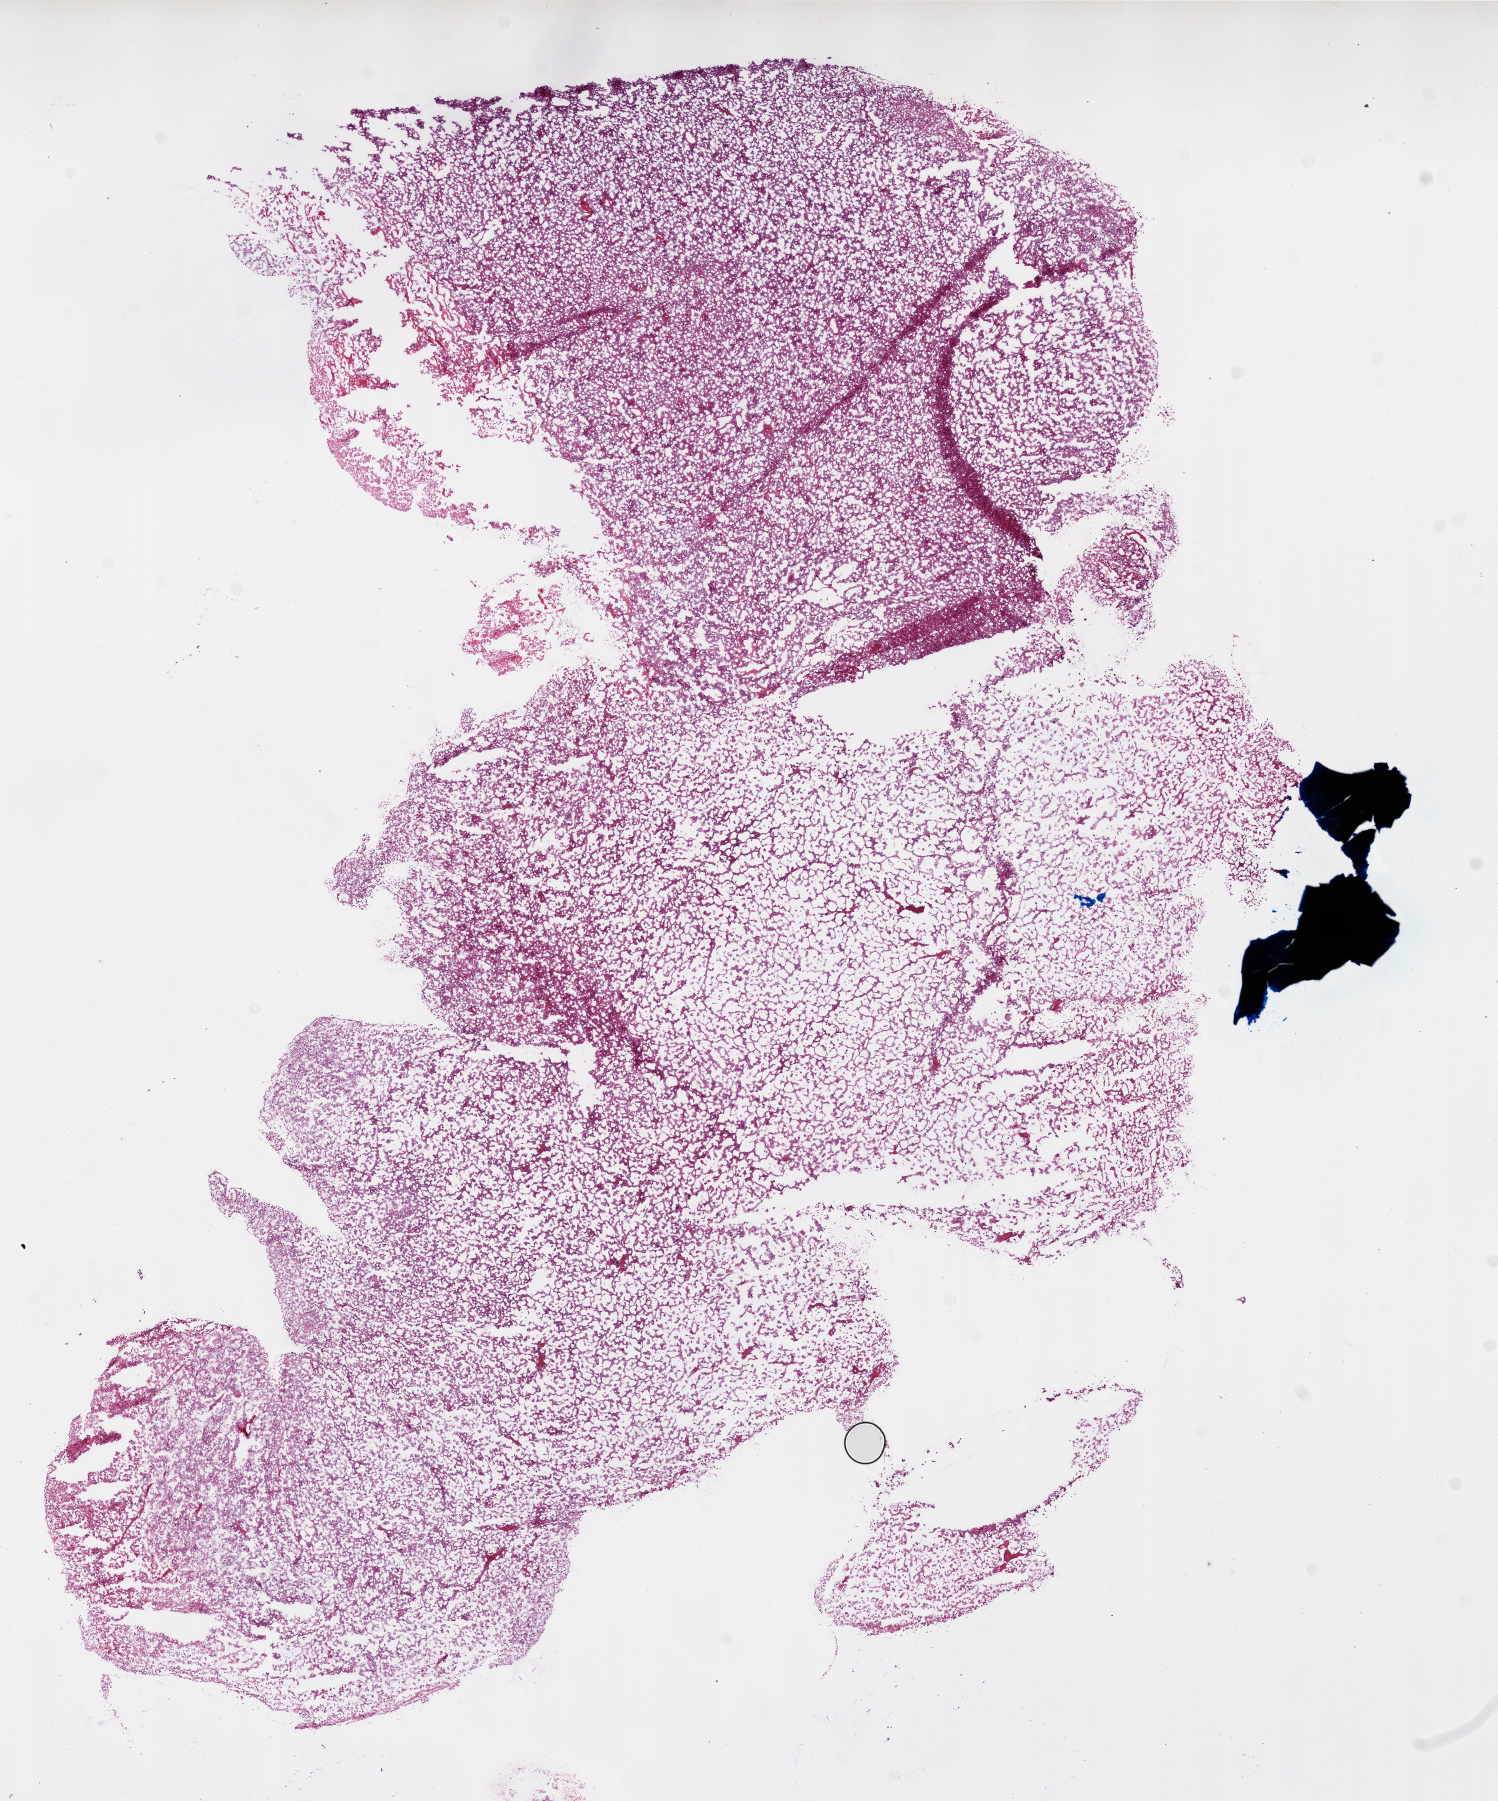
Digitized Hematoxylin and eosin (H&E) stained tissue section (whole slide) — whole scanned area (about 12.0 x 14.4 mm, slide scanned at 20x) shown as a low-resolution overview; frozen section from the top of the tissue portion; brain, primary tumour sample. Male patient; age at initial diagnosis 49 years.
Histologic diagnosis: Glioblastoma.